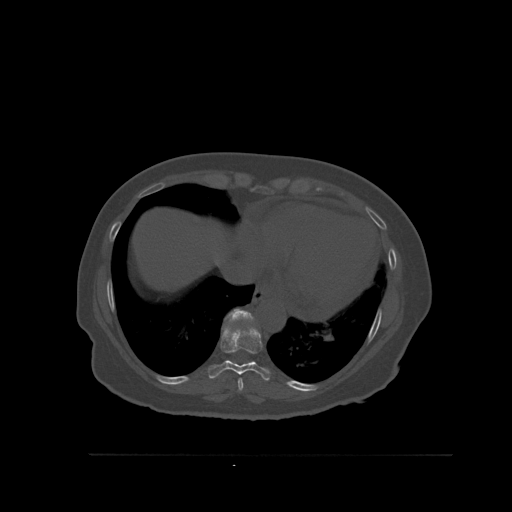
CT including the spine, one axial slice. Slice 334 of 527 in the series (ordered by position). Bone window (W 1800 / L 400 HU). 1.5 mm slice thickness. 512 × 512 image matrix, field of view 470 × 470 mm. Female patient, age 73 years. From the clinical record (not read from this slice): primary cancer: breast; vertebrae with lytic lesions (as recorded): L2.
Annotated regions visible in this slice (semi-automatic segmentation, software-assisted and operator-edited):
- T10 vertebra: bounding box <228,310,255,362> (left, top, right, bottom; pixels)
- T8 vertebra: <238,378,244,391>
- T9 vertebra: <208,324,270,381>